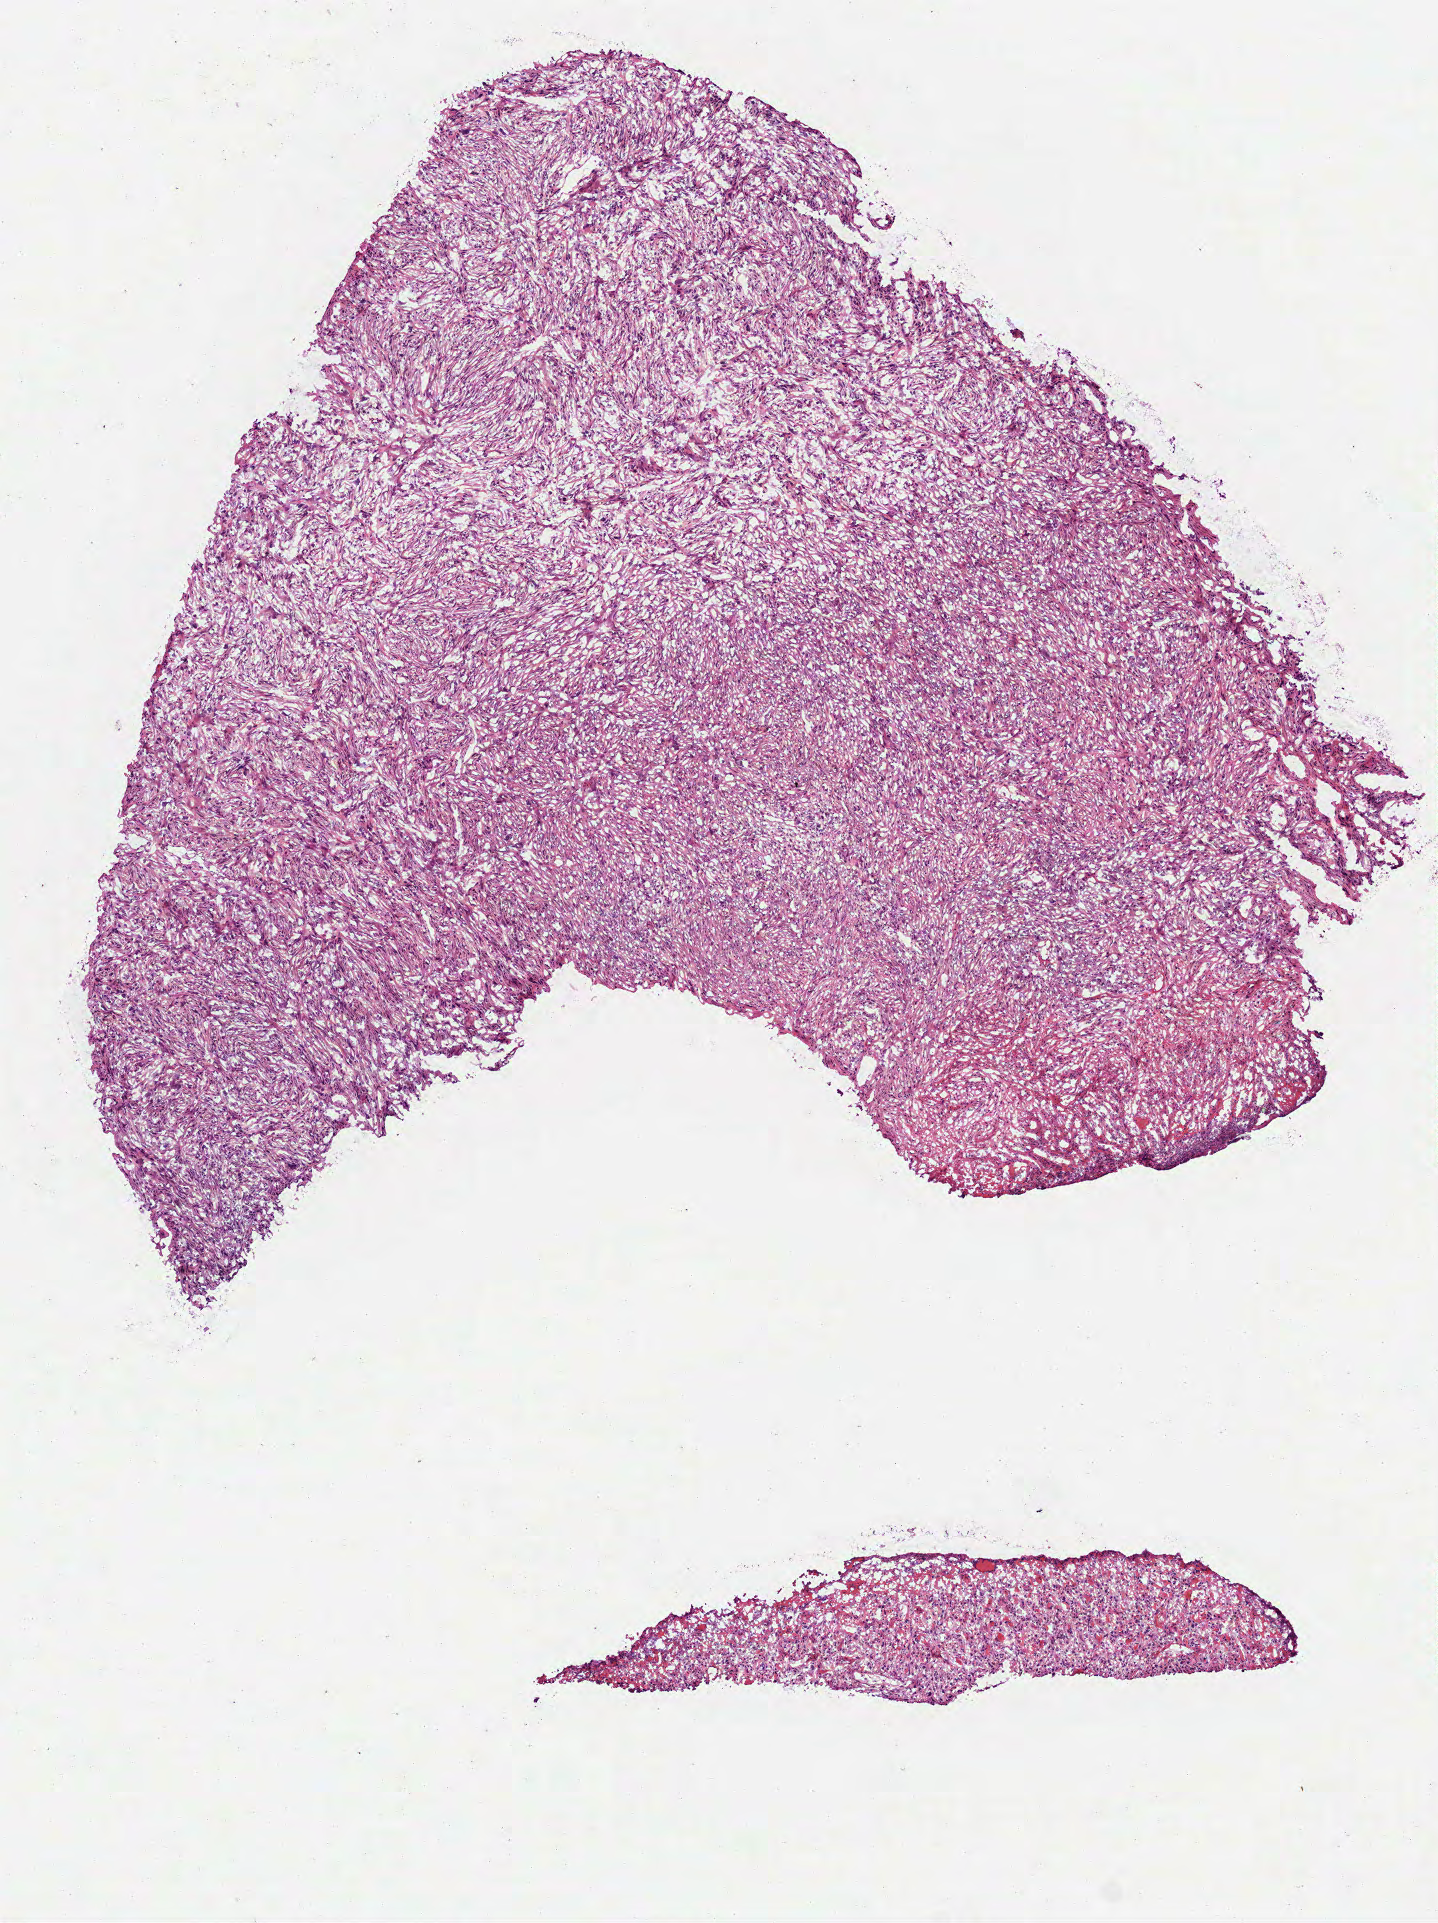
Digitized Hematoxylin and eosin (H&E) stained tissue section (whole slide) — low-resolution overview of the scanned area, about 5.8 x 7.8 mm (acquisition: 40x scan). Frozen section from the top of the tissue portion. Sample: primary tumour, head and neck. Male patient; age at initial diagnosis 79 years. Histologic grade: G3 (poorly differentiated). Composition of this section per pathologist review: tumour cells 92%, tumour nuclei 90%, normal cells 0%, stromal cells 5%, necrosis 3%. Inflammatory infiltration, as recorded: lymphocyte infiltration 2%.
Histologic diagnosis: Squamous cell carcinoma, NOS (tongue, NOS).